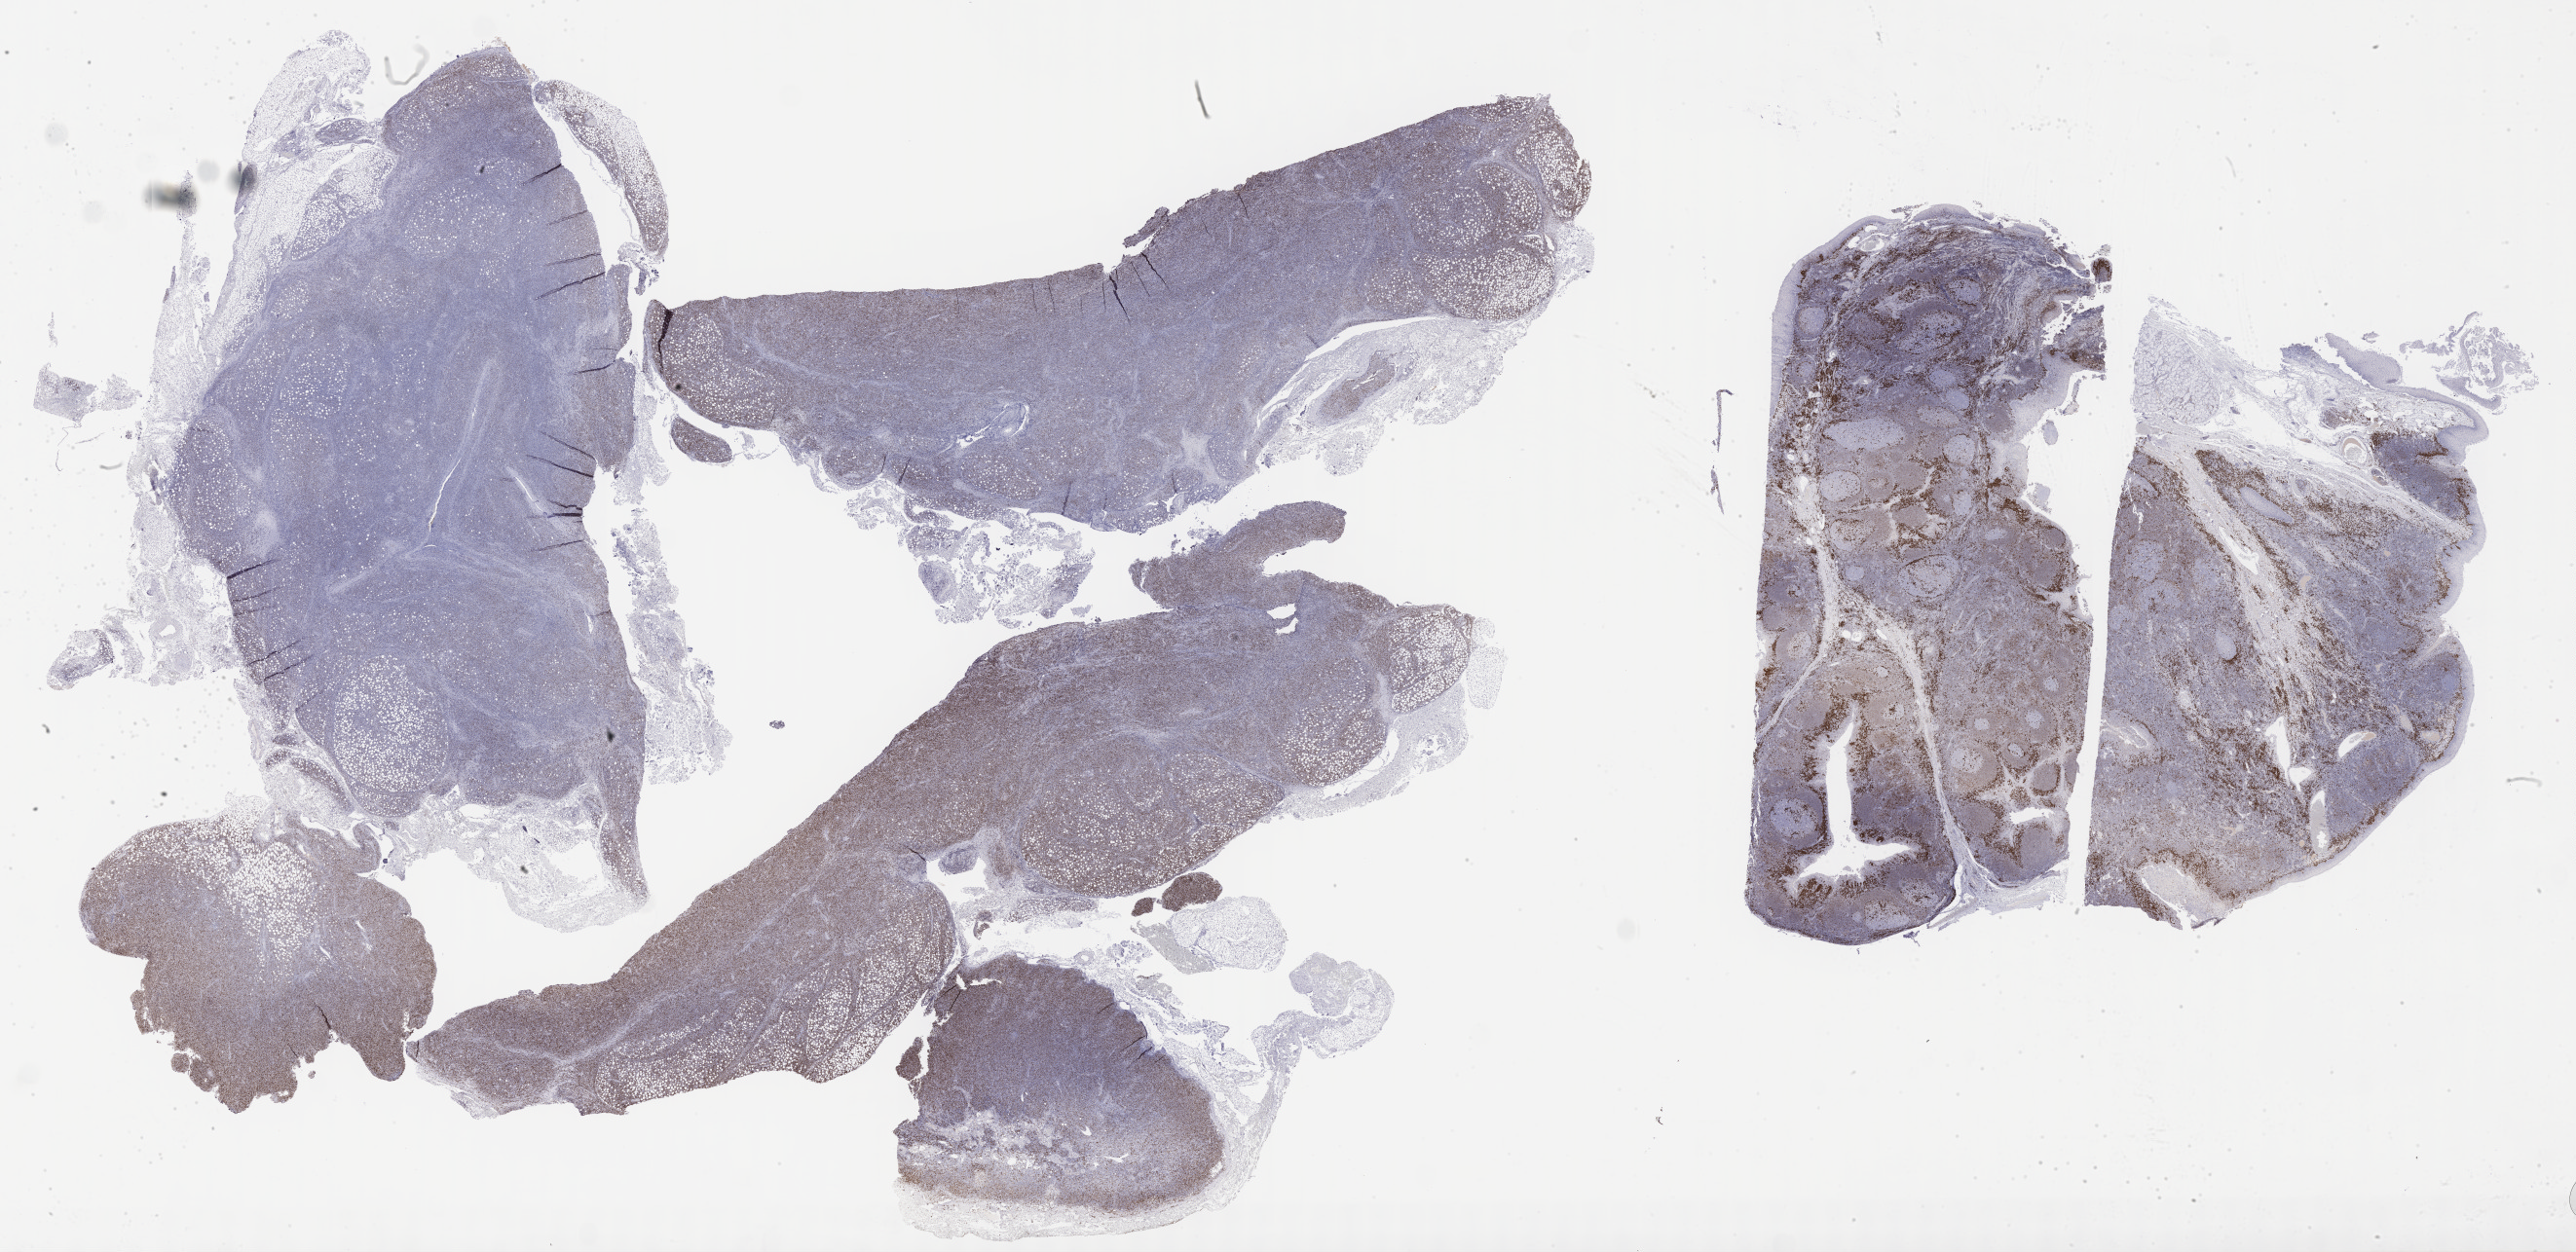
Immunohistochemistry (IHC) whole-slide image stained for IRF4/MUM1, a low-resolution overview of the entire scanned area, about 42.8 x 20.8 mm, tumor tissue, anatomic site: lymph node. Patient male; aged 68.
Diagnosis: Diffuse large B-cell lymphoma, NOS.